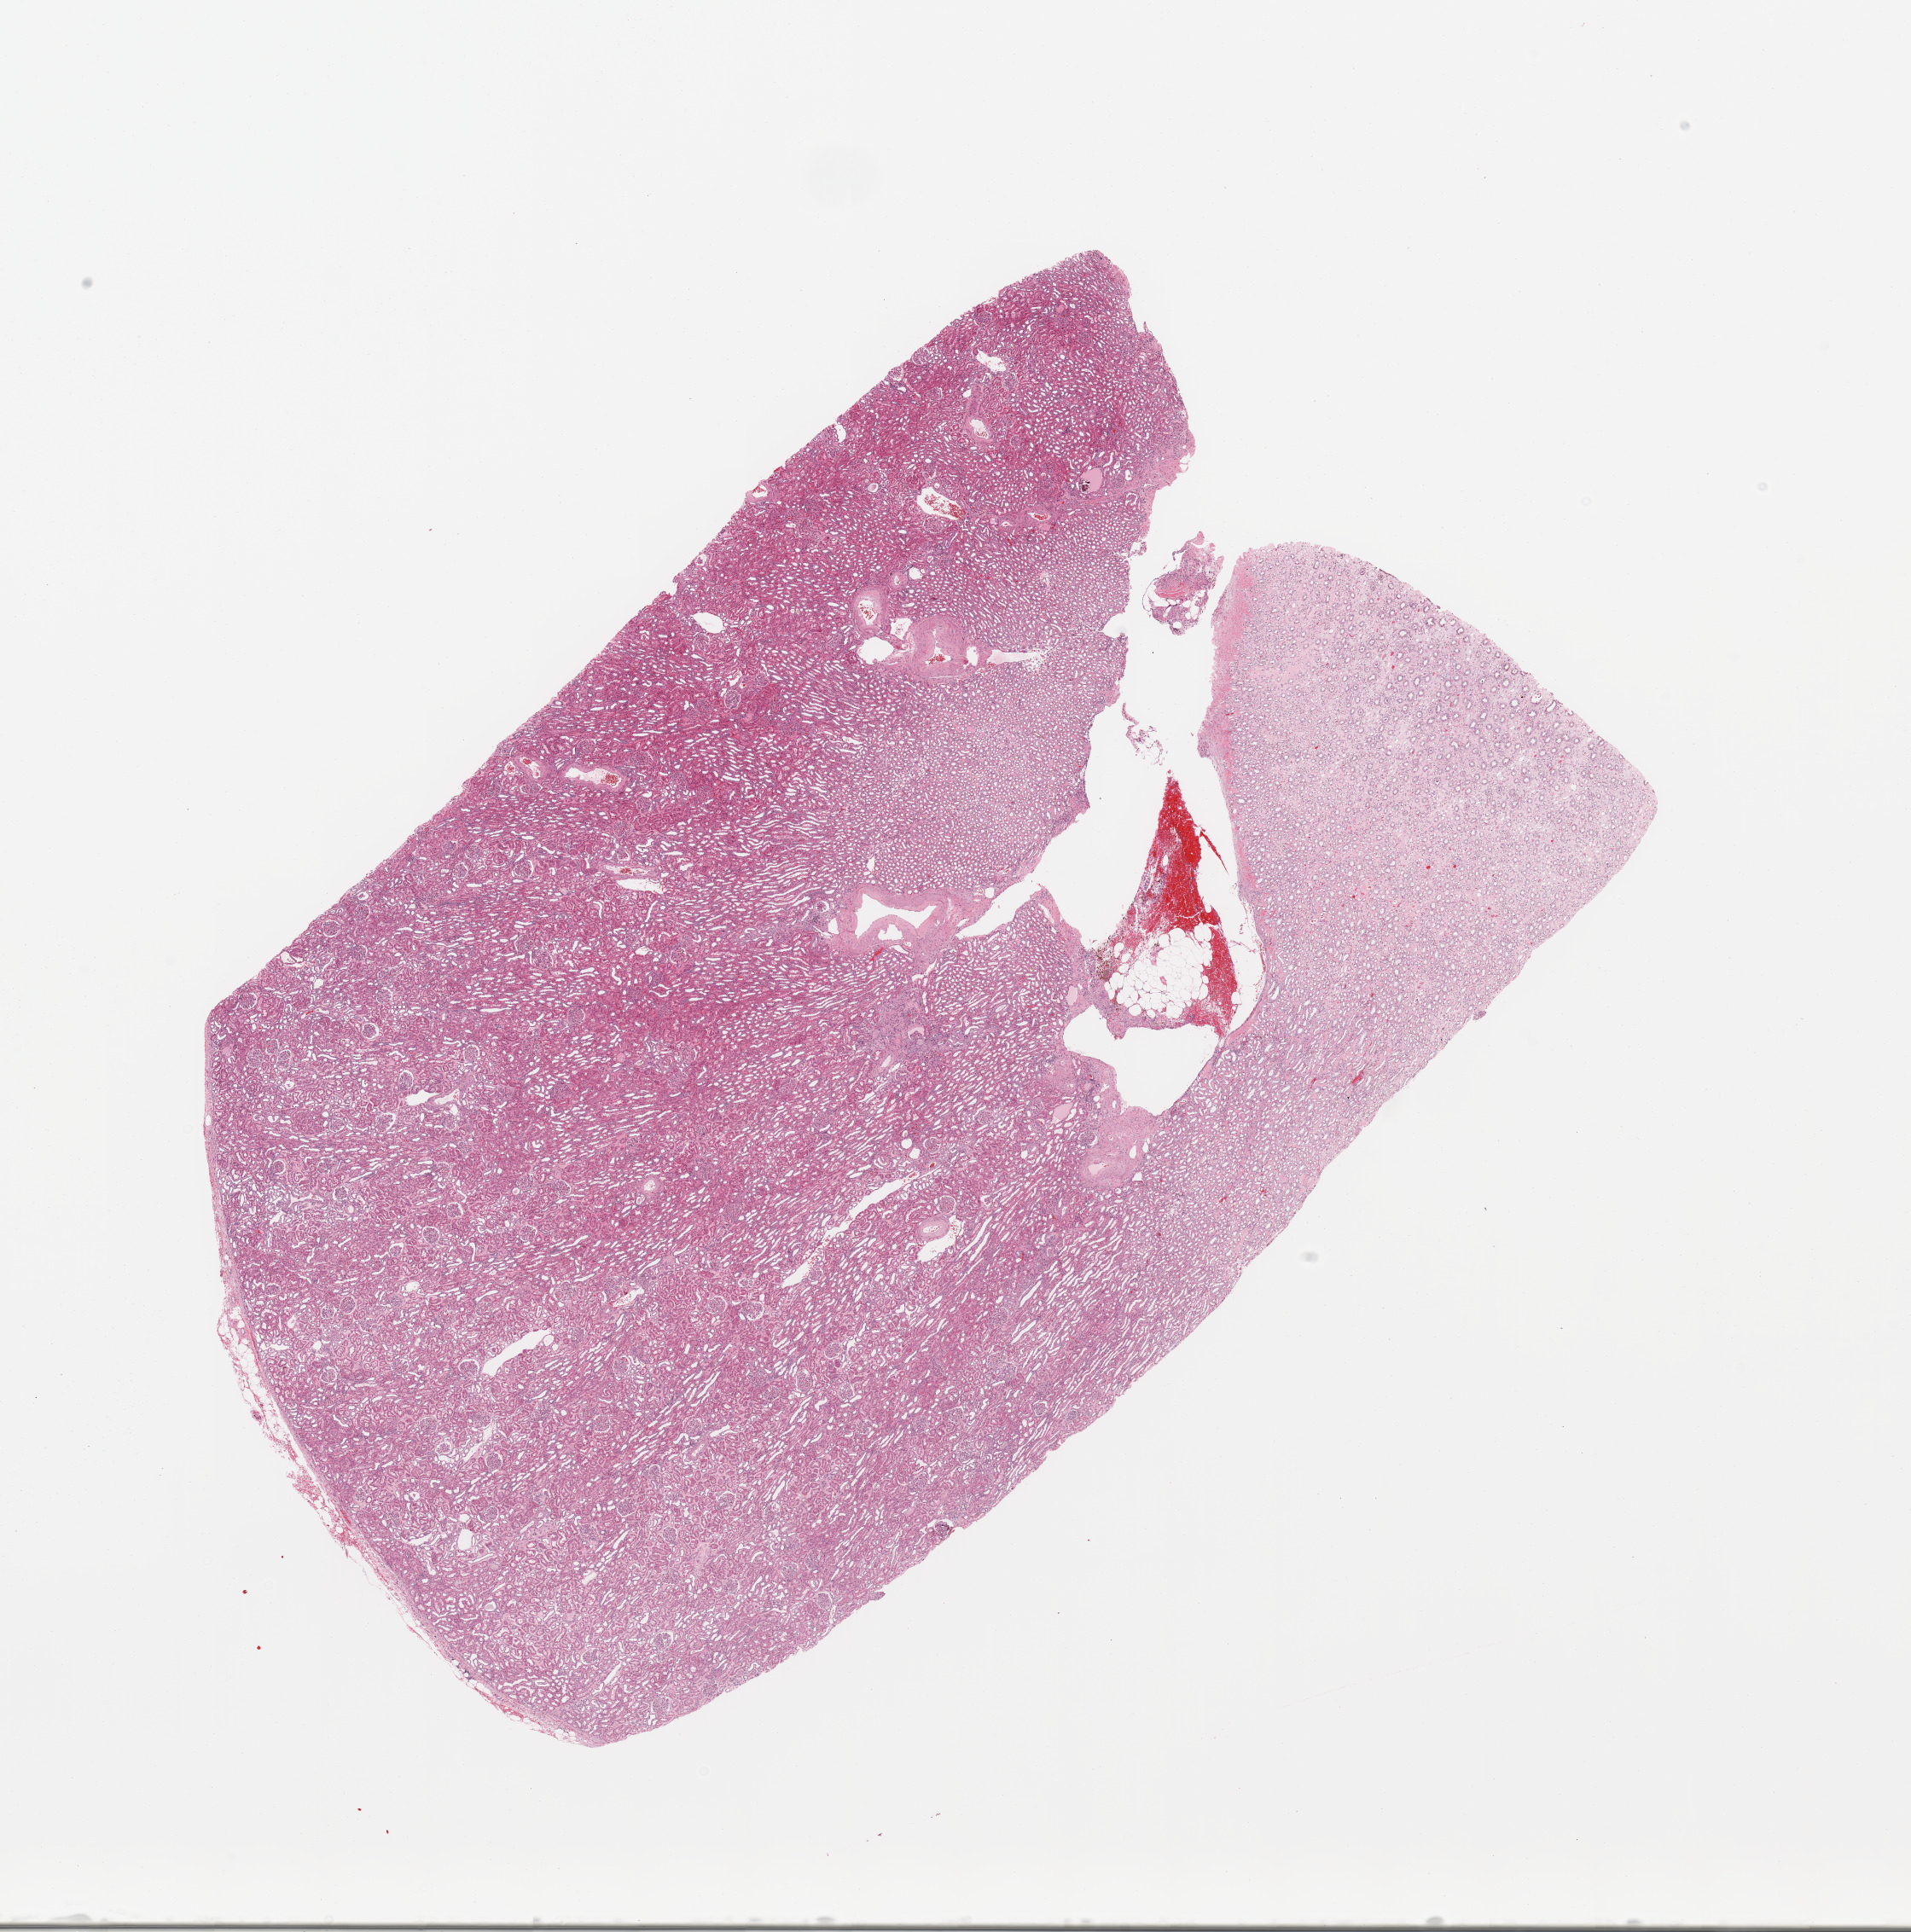
Whole-slide histology image, H&E-stained, shown as a low-resolution overview of the whole scanned area (about 17.7 x 17.9 mm), normal (non-tumour) tissue sample, sampled site: kidney. Female, 75 y/o.
This section: normal (non-tumour) tissue from the same patient. Patient diagnosis: Renal cell carcinoma, NOS.